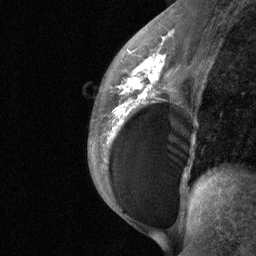
Breast MRI (dynamic contrast-enhanced), one sagittal slice; slice 38 of 64 in the series (ordered by position); dynamic contrast-enhanced study with each time point stored as its own series, time point 2 of 3 at this slice position (early post-contrast, ordered by acquisition time); 1.5 T; TE 4.8 ms, TR 27 ms; 2 mm slice thickness; 256 × 256 image matrix, field of view 200 × 200 mm. Female patient, age 34 years. From the clinical record (not read from this slice): setting: breast cancer imaged before/during neoadjuvant chemotherapy; receptor status: HR-positive, HER2-negative.
Annotated regions visible in this slice (semi-automatic segmentation, software-assisted and operator-edited):
- analysis volume of interest (the breast-tissue region the enhancement analysis was run in; not a lesion): box from (x=92, y=50) to (x=188, y=185) px
- tumour enhancement mask (voxels above the 90 % enhancement threshold inside the analysis volume of interest): (x=114, y=55)–(x=165, y=124)